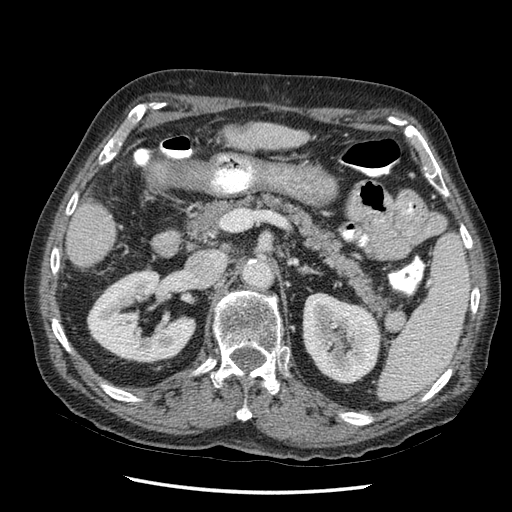
Contrast-enhanced abdominal CT (liver protocol), one axial slice. Reconstruction kernel STANDARD. 120 kVp. Soft-tissue window (W 400 / L 40 HU). 2.5 mm slice thickness. 512 × 512 image matrix, field of view 360 × 360 mm. Case-level facts recorded for this patient, not image findings: diagnosis: hepatocellular carcinoma (patient treated with transarterial chemoembolisation; whether this scan precedes or follows treatment is not stated here); TNM stage (as recorded): Stage-I; Child-Pugh class: A; tumour differentiation: moderately differentiated.
Outlined on this slice (semi-automatic segmentation, software-assisted and operator-edited):
- liver parenchyma outside the tumour (the mass and vessels are separate outlines, so this box may not span the whole liver): bounding box <206,120,314,158> (left, top, right, bottom; pixels)